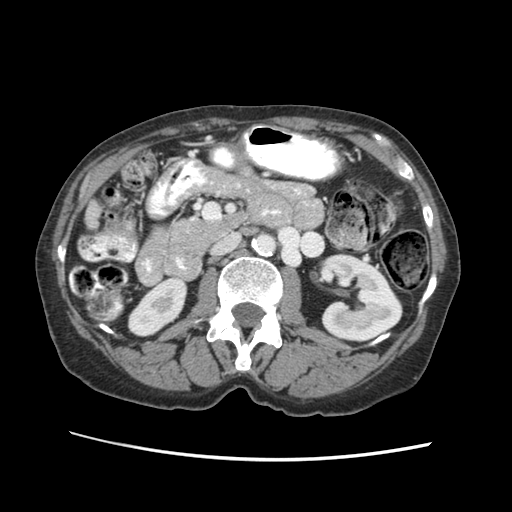
Contrast-enhanced abdominal CT (liver protocol), one axial slice; slice 6 of 63 in the series (ordered by position); soft-tissue window (W 400 / L 40 HU); 2.5 mm slice thickness; 512 × 512 image matrix, field of view 340 × 340 mm. Case-level facts recorded for this patient, not image findings: diagnosis: hepatocellular carcinoma (patient treated with transarterial chemoembolisation; whether this scan precedes or follows treatment is not stated here); TNM stage (as recorded): Stage-I; Child-Pugh class: B; tumour differentiation: well differentiated; tumour nodularity: uninodular.
Annotated regions visible in this slice (semi-automatically segmented with operator editing):
- liver parenchyma outside the tumour (the mass and vessels are separate outlines, so this box may not span the whole liver): bounding box <80,202,100,250> (left, top, right, bottom; pixels)